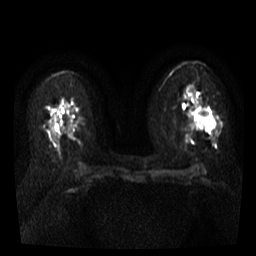
Breast MRI, one axial slice; slice 16 of 35 in the series (ordered by position); diffusion-weighted series; image 2 of 4 stored at this slice position (different b-values; order by instance number); 3 T; 5 mm slice thickness; 256 × 256 image matrix. Female patient.
Annotated regions visible in this slice (manually delineated by an expert):
- tumour on diffusion-weighted imaging: bounding box <193,106,217,129> (left, top, right, bottom; pixels)